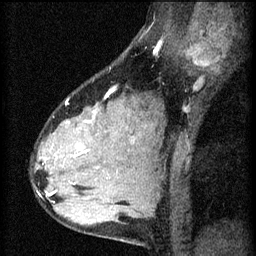
Breast MRI (dynamic contrast-enhanced), one sagittal slice. Position 42 of 60 along the scan axis. 3 images stored at this slice position (order not interpretable as contrast timing). 1.5 T. TE 4.2 ms, TR 8.2 ms. 2 mm slice thickness. 256 × 256 image matrix, field of view 180 × 180 mm. Female patient, age 37 years.
Structures marked on this image (semi-automatically segmented with operator editing):
- analysis volume of interest (the breast-tissue region the enhancement analysis was run in; not a lesion): box from (x=44, y=102) to (x=119, y=197) px
- tumour enhancement mask (voxels above the 70 % enhancement threshold inside the analysis volume of interest): (x=48, y=110)–(x=97, y=195)